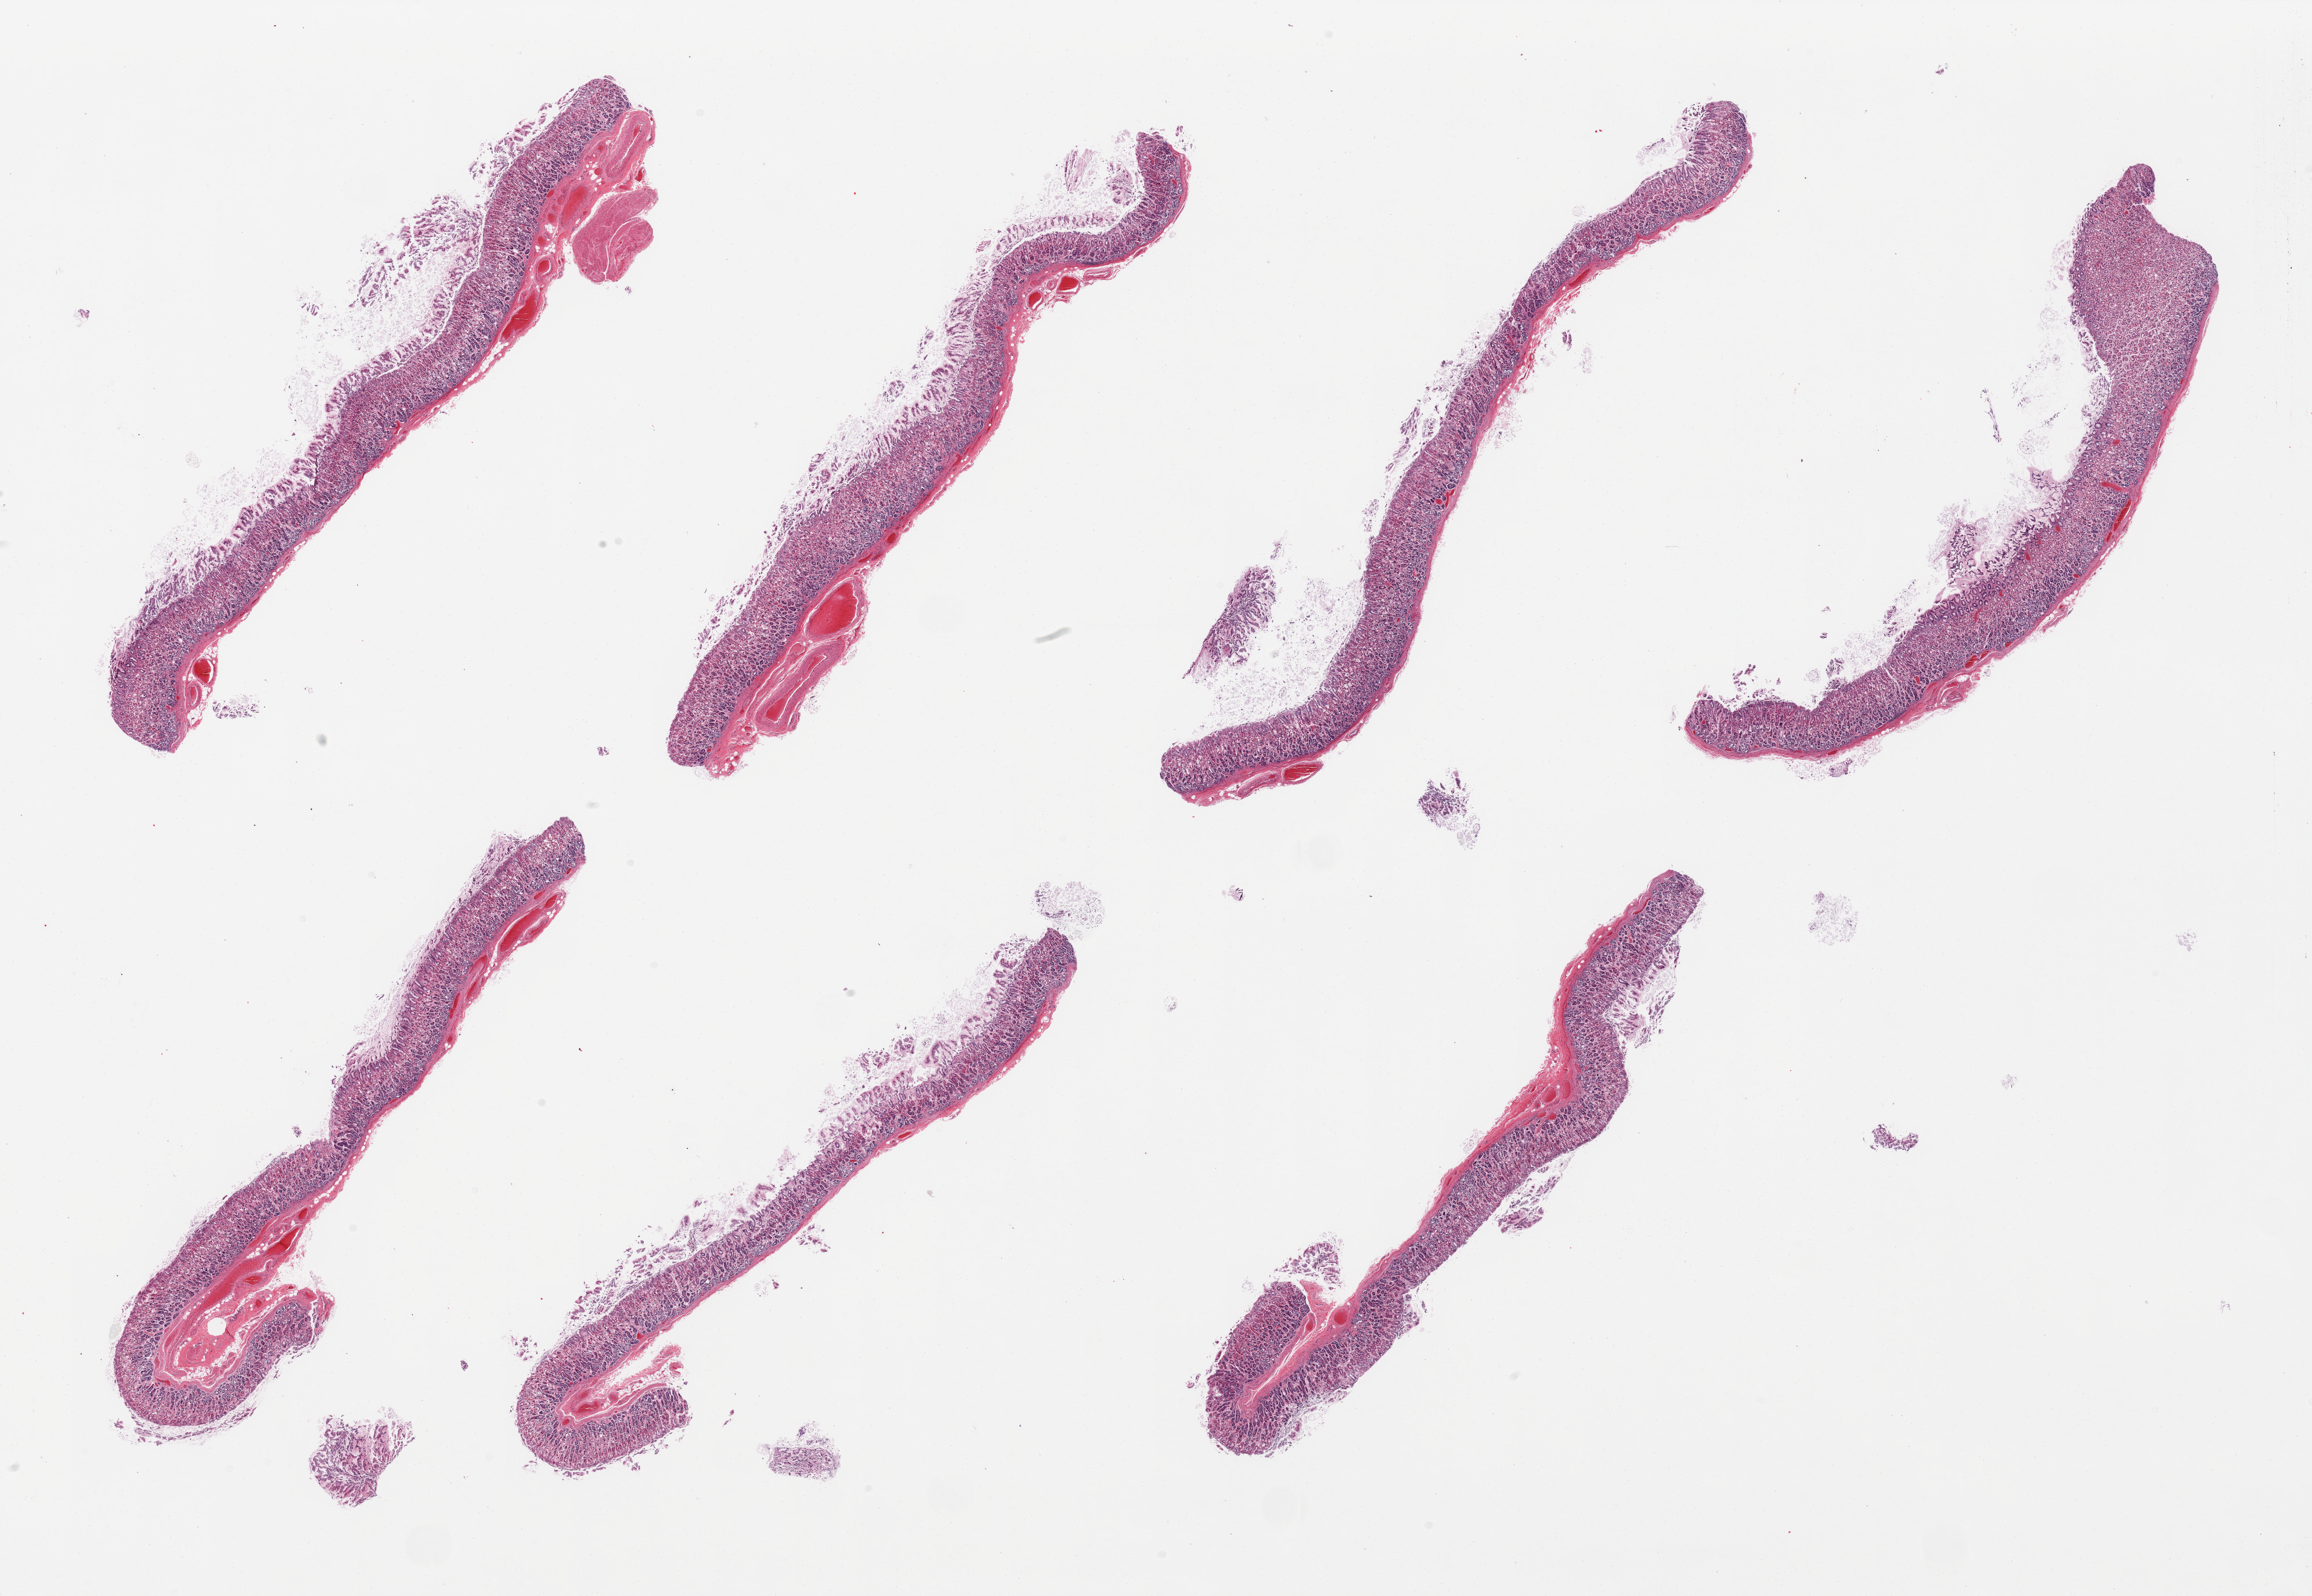
Digitized H&E-stained section, low-resolution overview of the scanned area, about 31.5 x 21.7 mm (from a 20x scan); PAXgene-fixed, paraffin-embedded tissue; section of stomach (target tissue); tissue donor sample.
* pathologist's review note for this sample: 7 pieces; well dissected mucosa